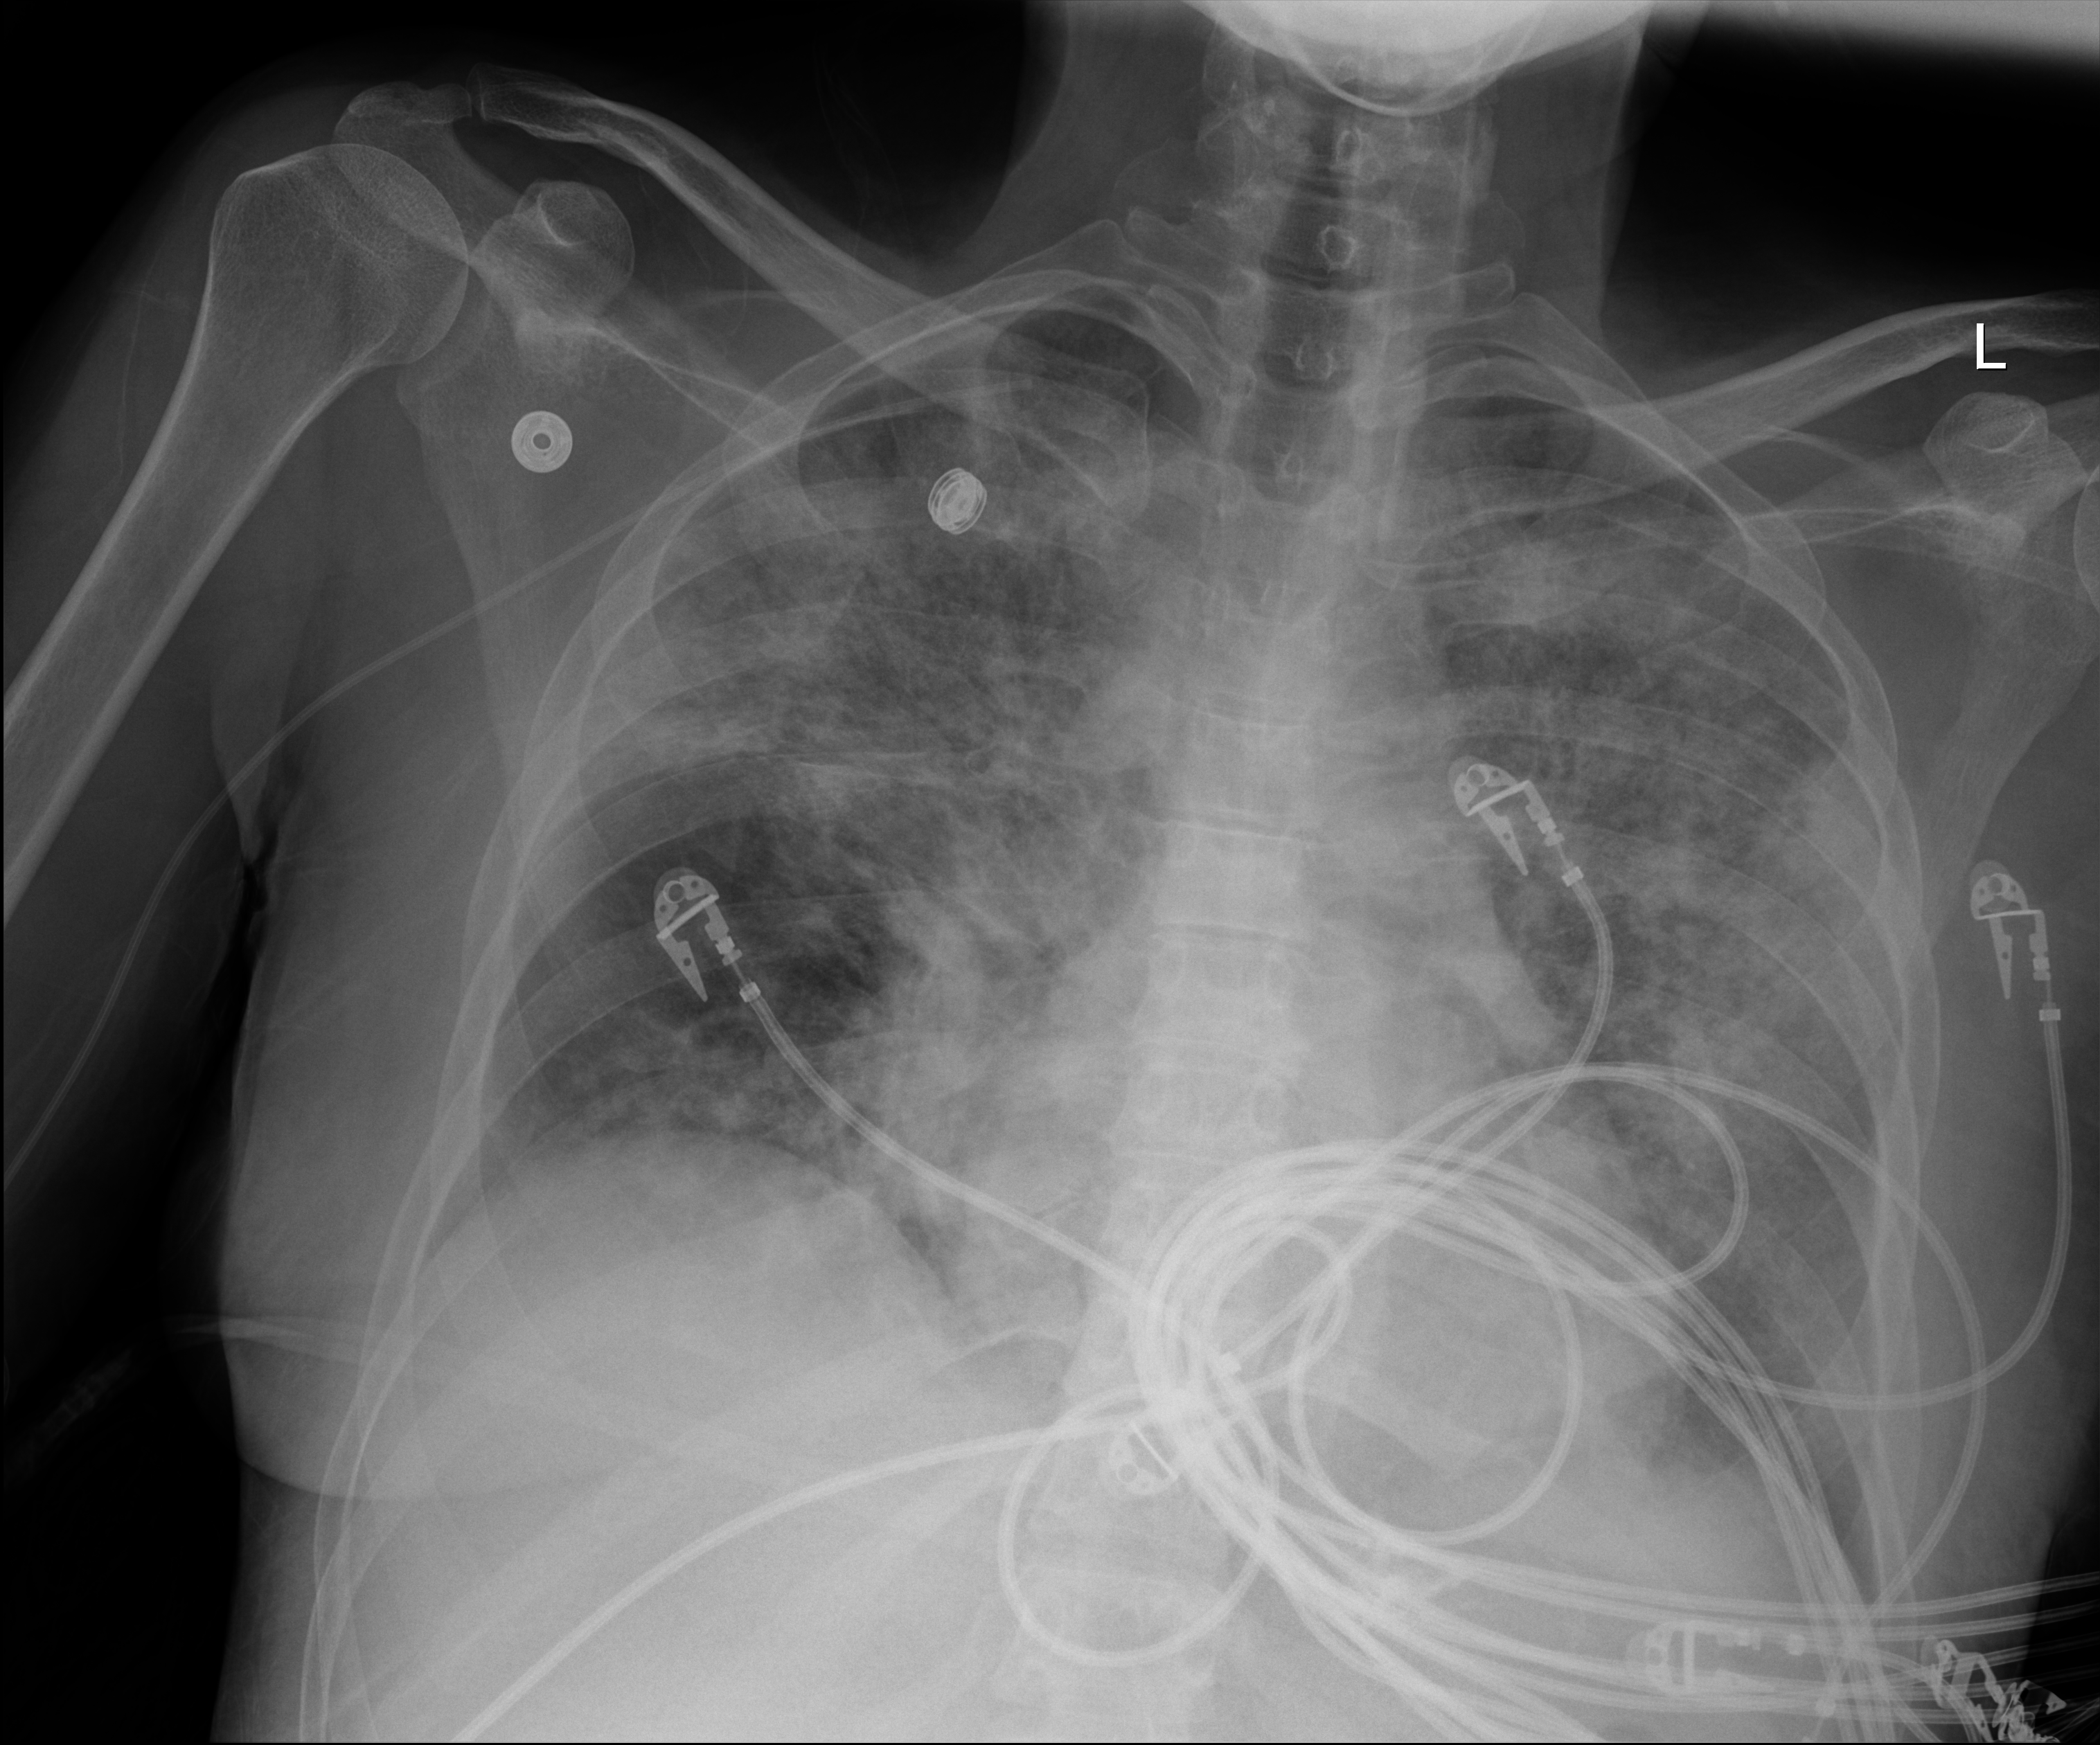
Bedside chest radiograph (digital radiography), anteroposterior (AP) projection. Patient hospitalised with COVID-19; female, aged 18–59 years.
Hospital-stay facts (about this admission, not read from this image; timing relative to this image not recorded):
- admitted to intensive care during this hospital stay: yes
- COPD (admission record): no
- length of hospital stay: 27 days